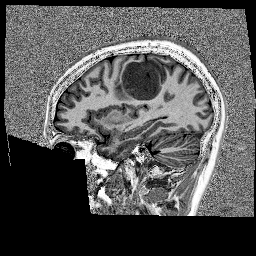
Brain MRI from a brain-tumour surgery series, one sagittal slice; slice 58 of 176 in the series (ordered by position); 1 mm slice thickness; 256 × 256 image matrix. From the clinical record (not read from this slice): histopathology: Glioblastoma; WHO grade: 4; IDH mutation: no.
Outlined on this slice (outlined manually by an expert reader):
- tumour: bounding box <118,58,175,105> (left, top, right, bottom; pixels)